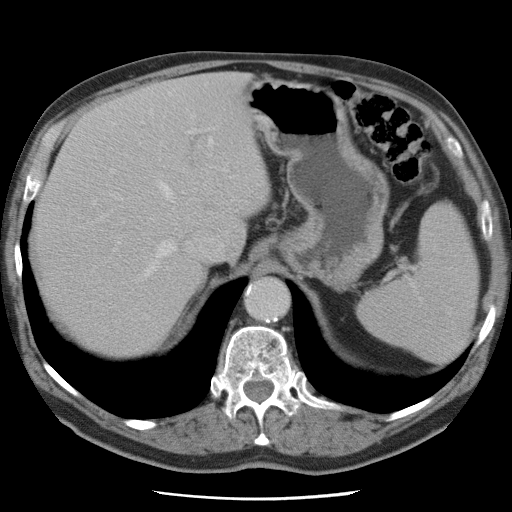
Contrast-enhanced abdominal CT, one axial slice; slice 57 of 78 in the series (ordered by position); 120 kVp; intravenous contrast given; soft-tissue window (W 400 / L 40 HU); 5 mm slice thickness; 512 × 512 image matrix, field of view 337 × 337 mm. Male patient, age 75 years. Case-level facts recorded for this patient, not image findings: diagnosis: colorectal cancer liver metastases, imaged before liver resection; multiple liver metastases: yes; largest metastasis: 2.4 cm; chemotherapy before resection: yes.
Structures marked on this image (expert manual segmentation):
- hepatic veins: bounding box [x1, y1, x2, y2] px = [93, 128, 212, 279]
- liver: [36, 74, 269, 353]
- planned liver remnant (the part of the liver to remain after resection): [36, 131, 204, 353]
- portal vein (with intrahepatic branches): [110, 170, 126, 253]